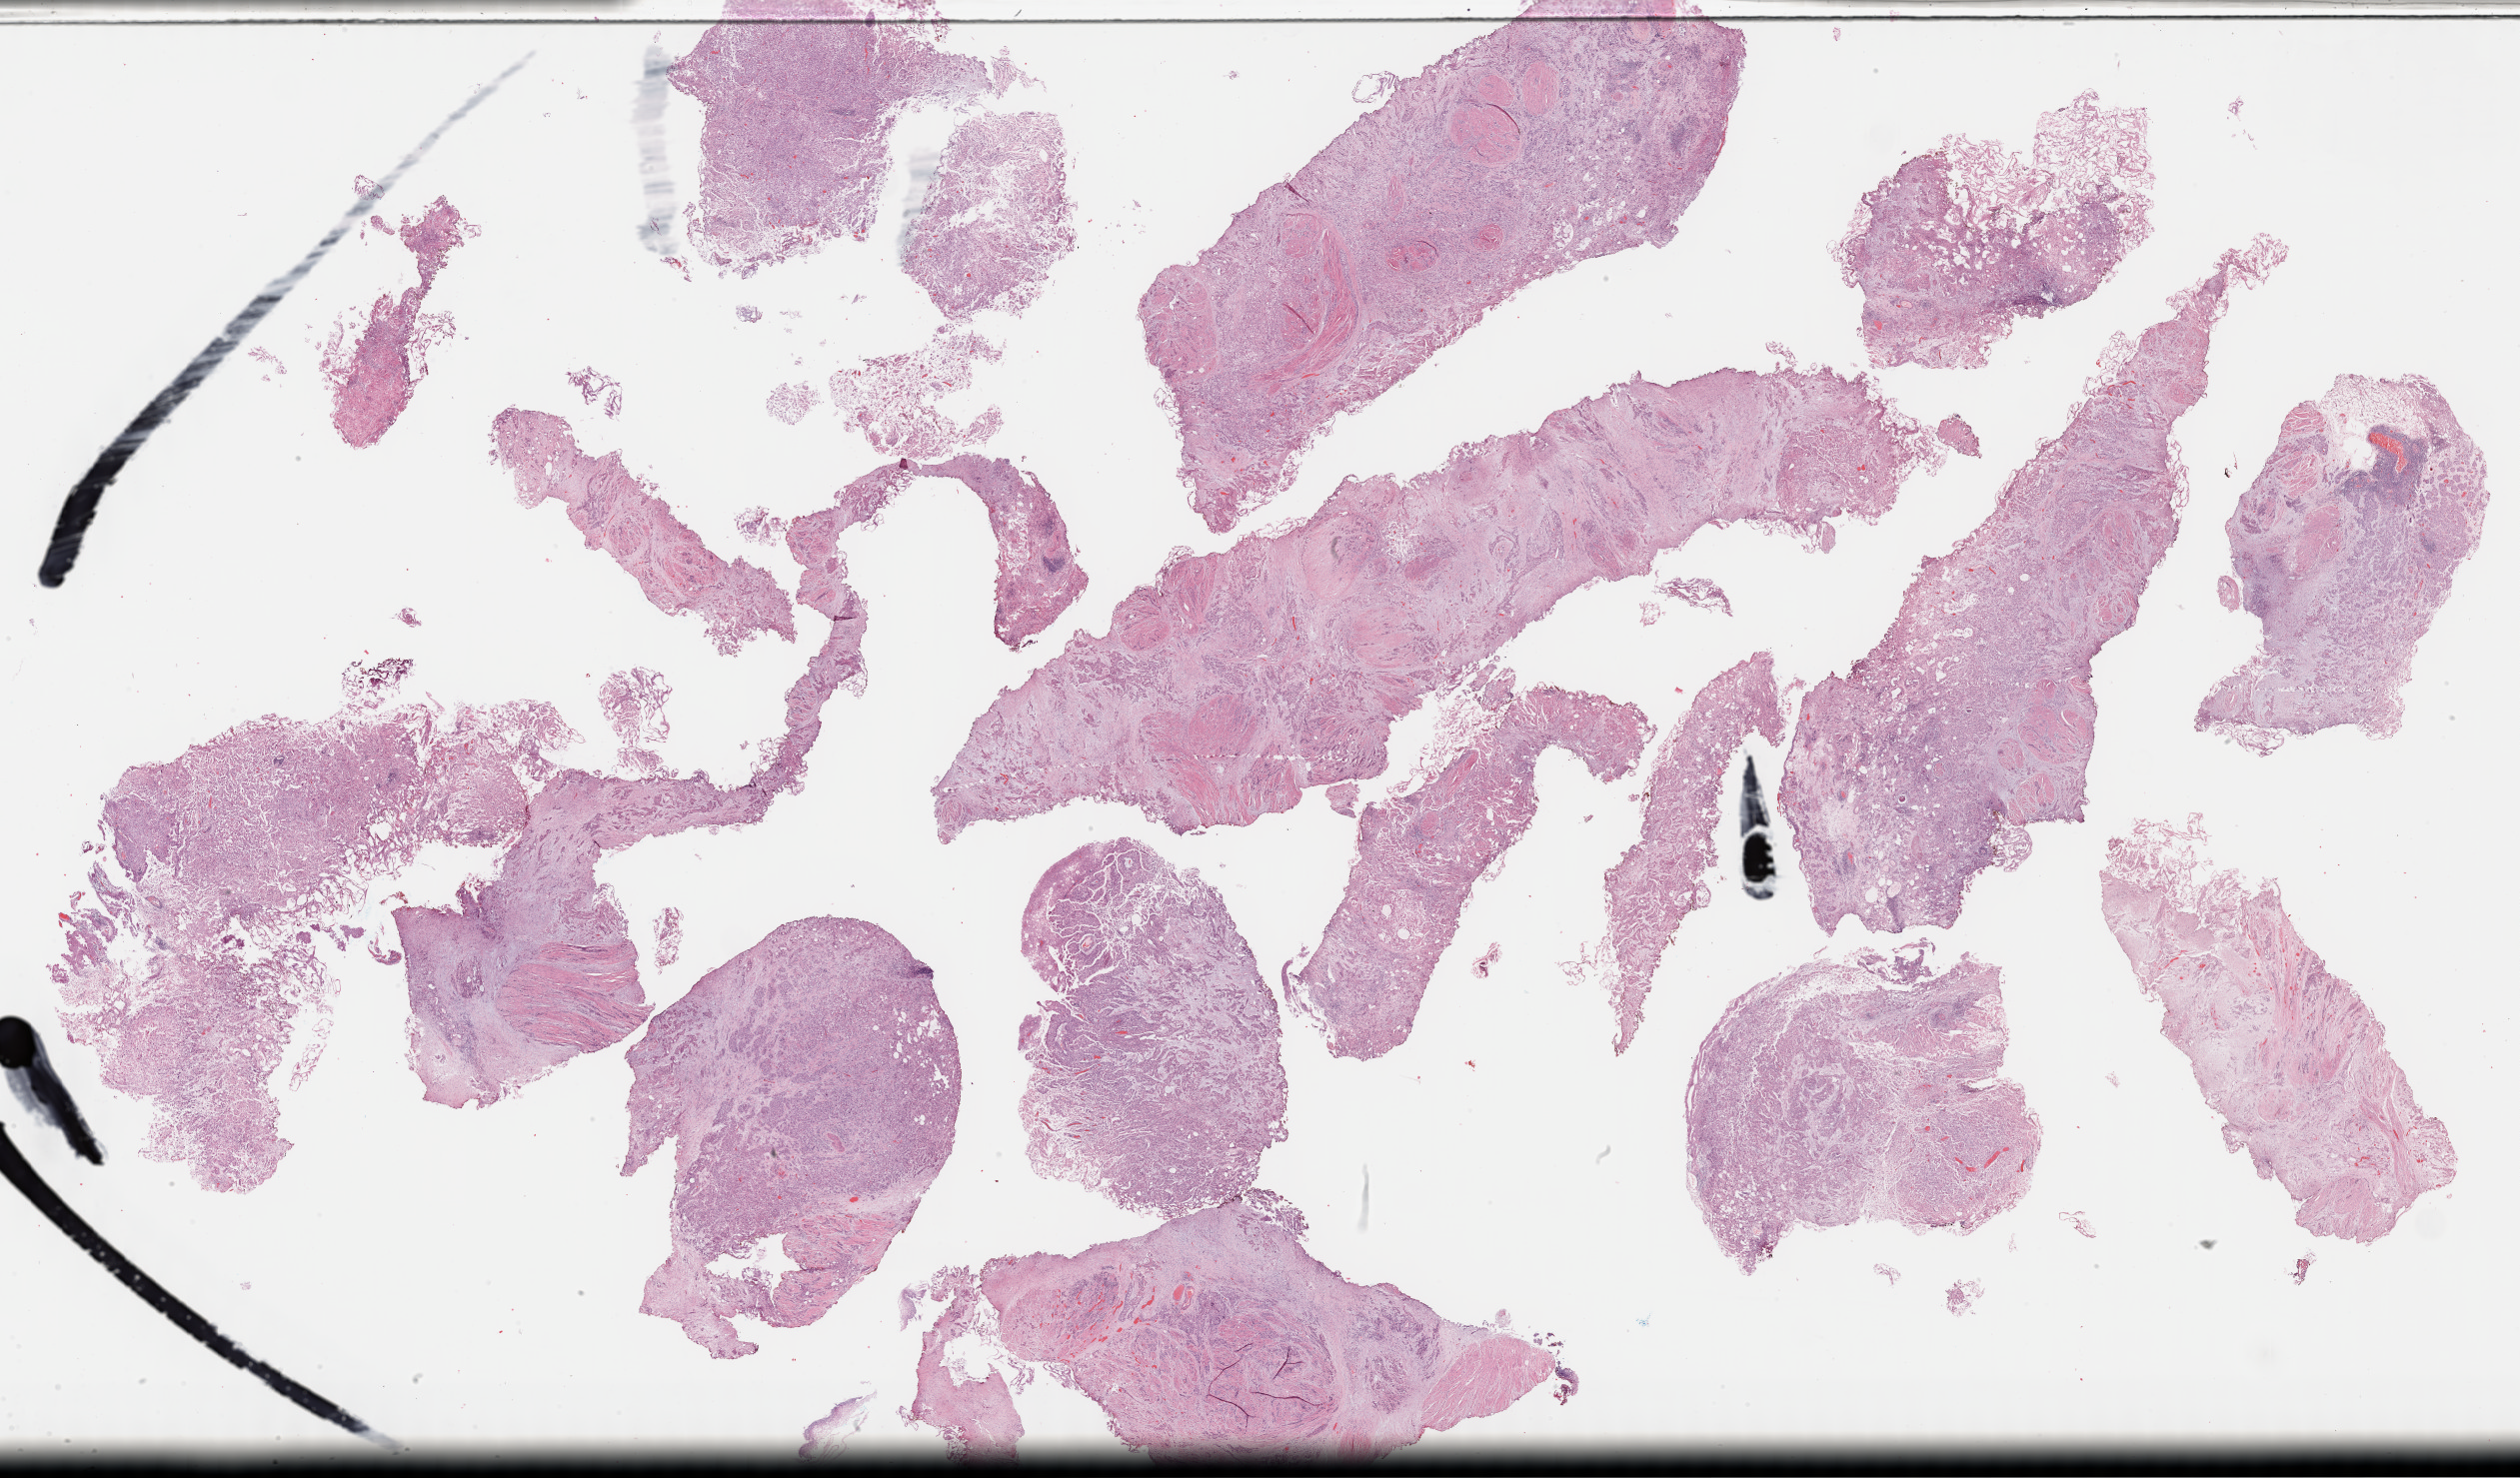
H&E-stained whole-slide image, whole scanned area (about 40.8 x 23.9 mm) shown as a low-resolution overview, formalin-fixed paraffin-embedded (FFPE) diagnostic section, sample: primary tumour, bladder. Patient: female, age at initial diagnosis 53 years. Histologic grade: high grade.
* TNM: T2 NX M0
* diagnosis: Transitional cell carcinoma
* AJCC pathologic stage: II (7th edition)